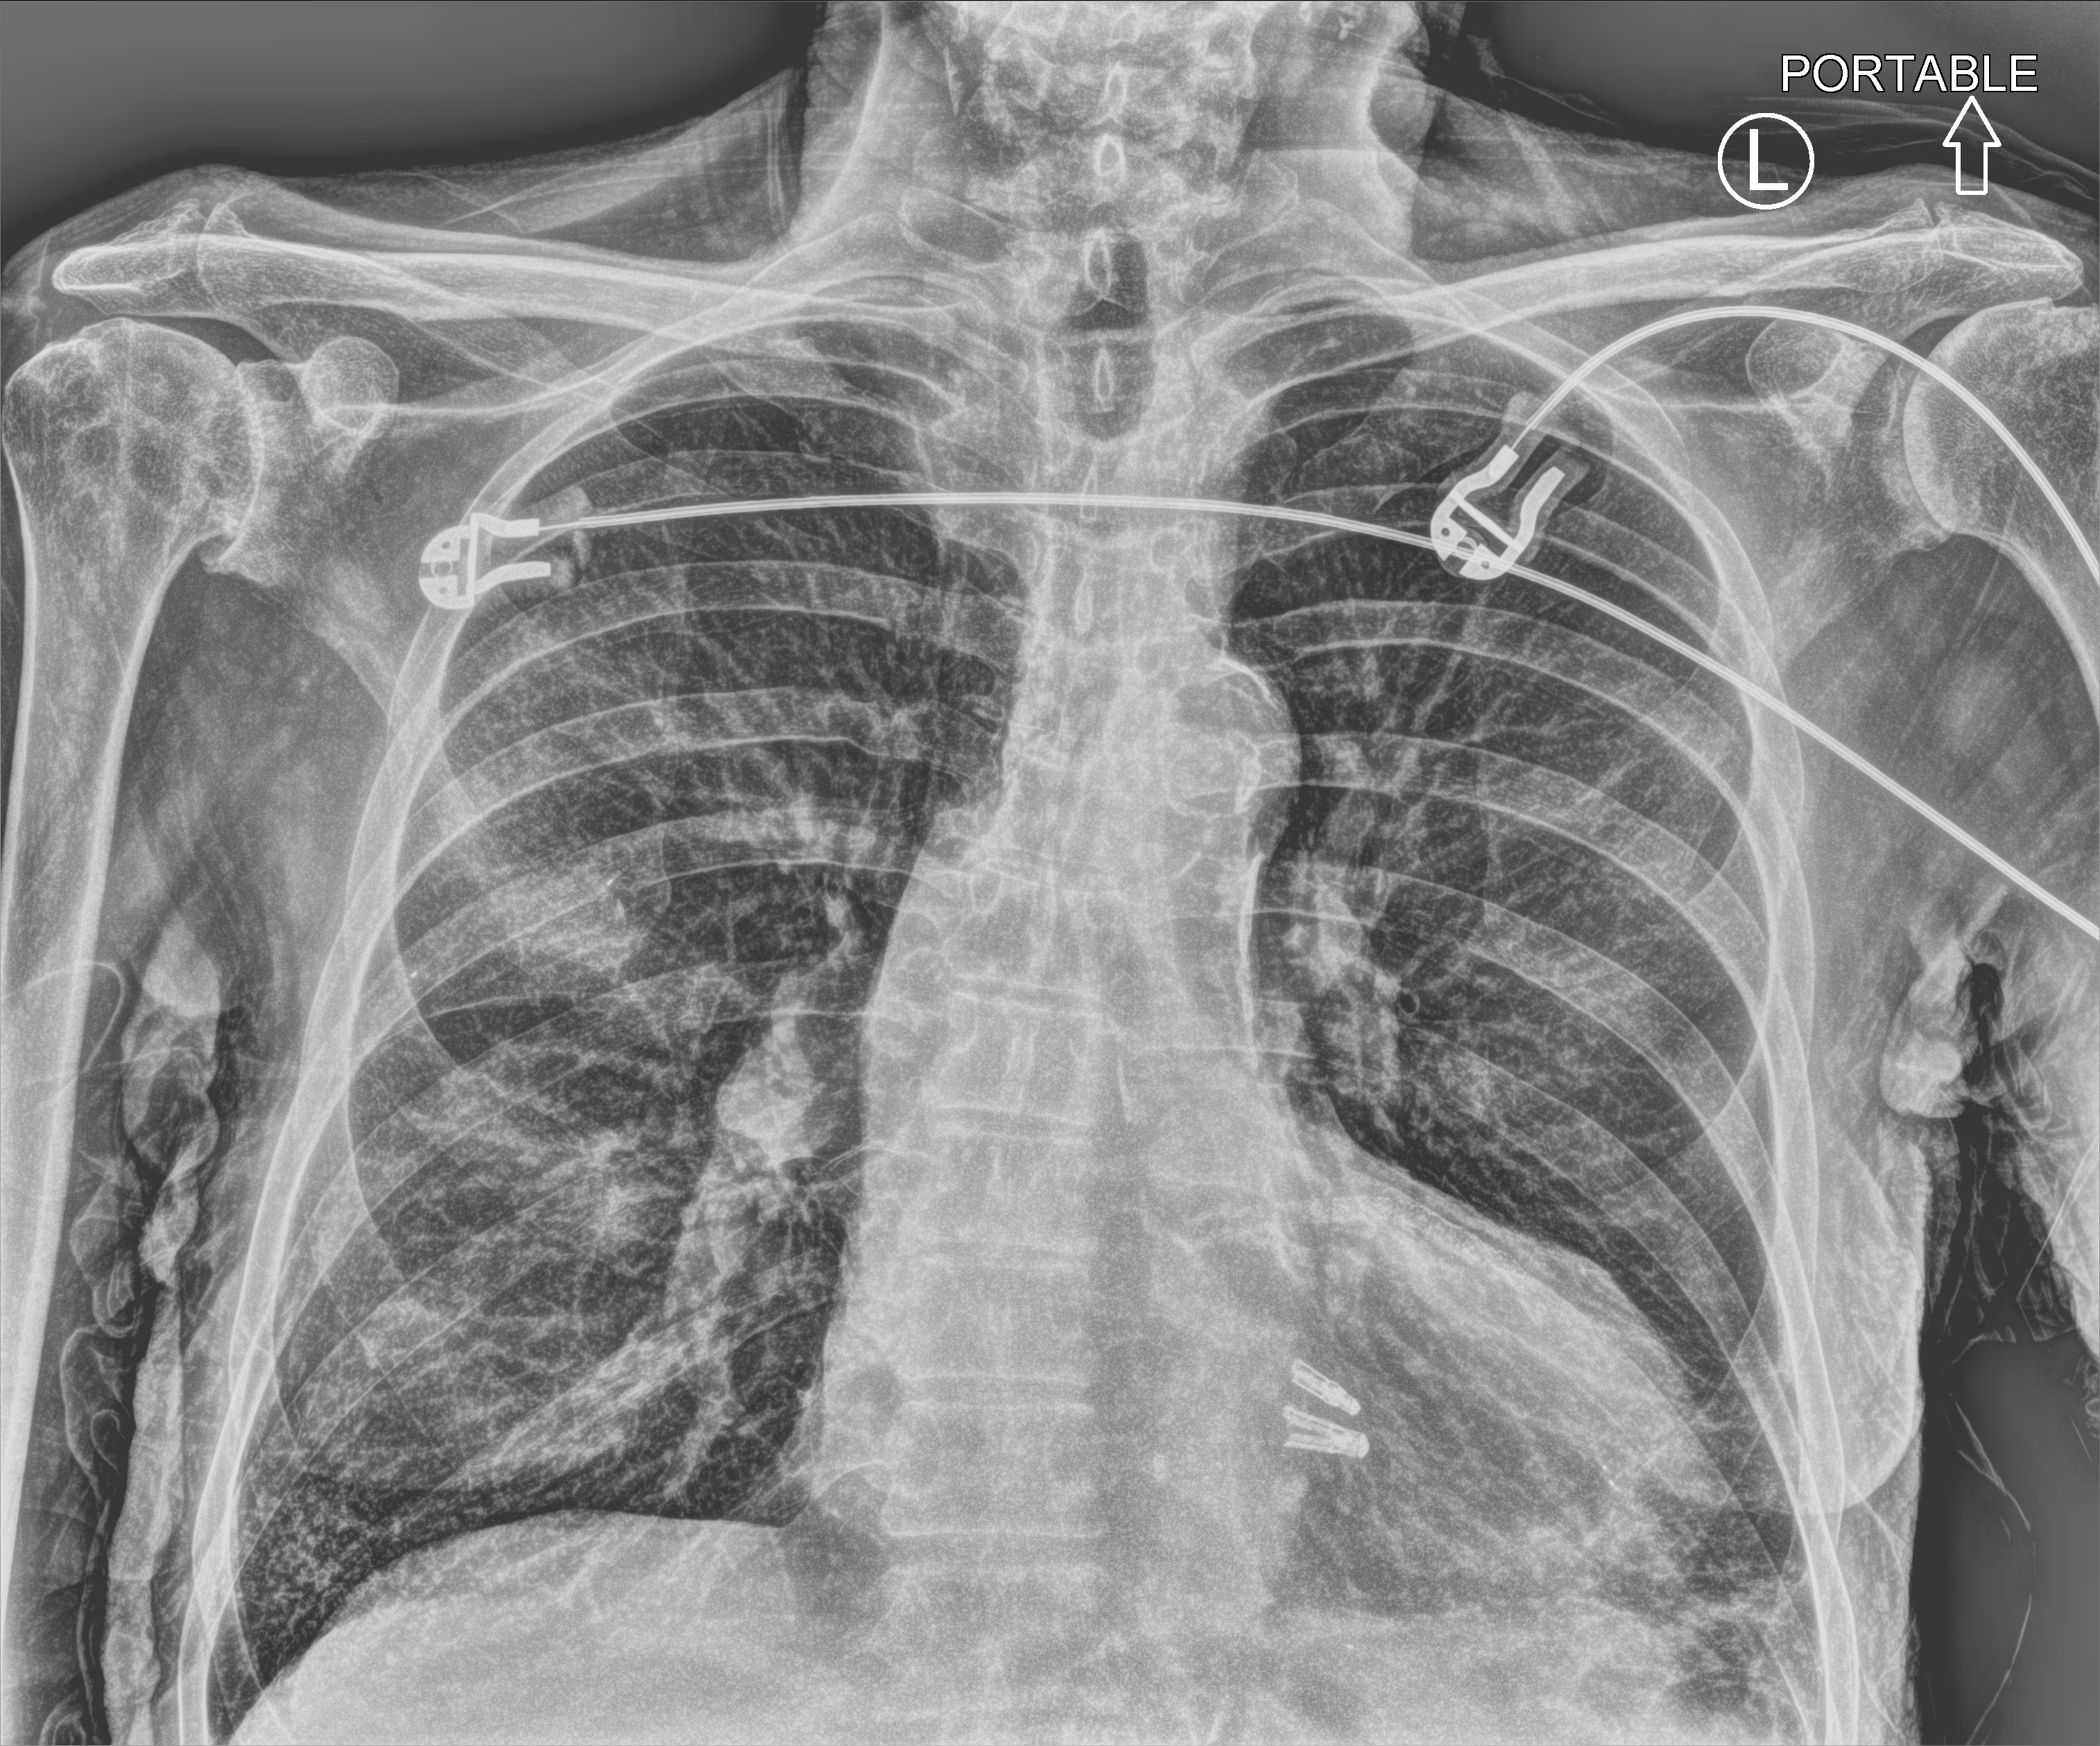
Bedside chest radiograph (computed radiography), anteroposterior (AP) projection. Patient hospitalised with COVID-19; male, aged 75–90 years.
From the hospital-stay record, not from the radiograph (when in the stay this image was taken is not recorded): admitted to intensive care during this hospital stay: no; mechanically ventilated during this hospital stay: no.